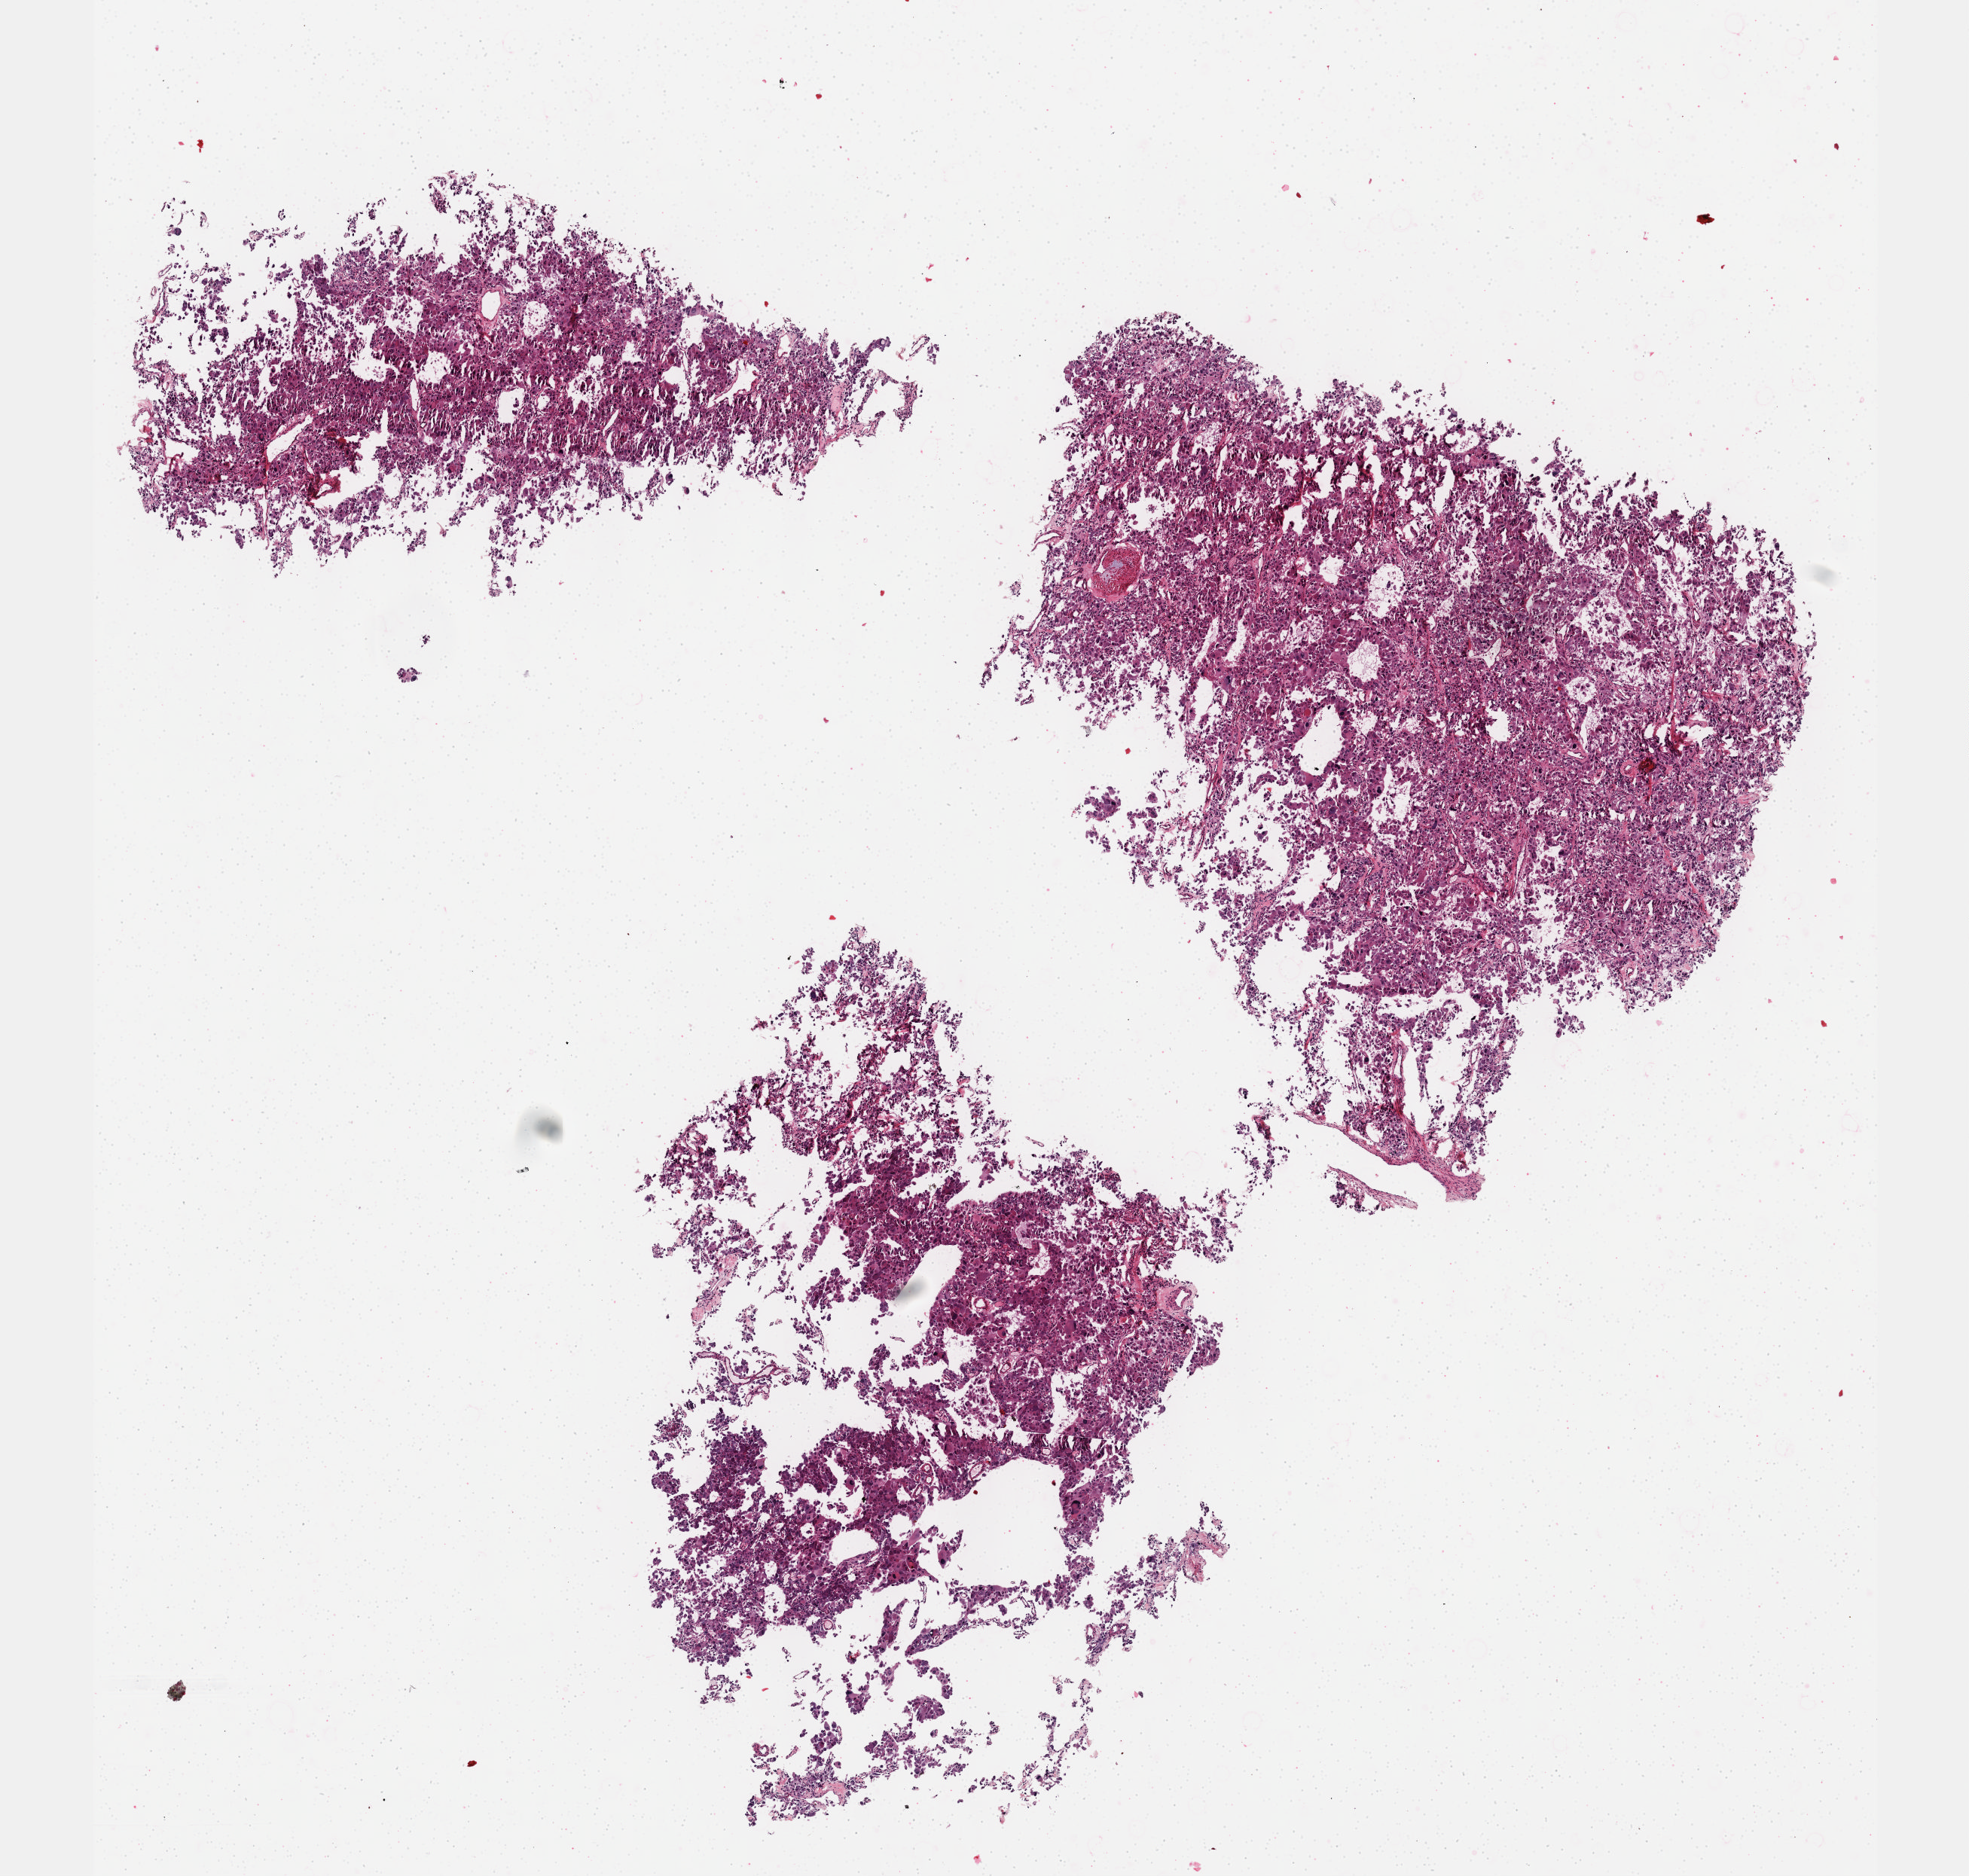
Digitized Hematoxylin and eosin (H&E) stained tissue section (whole slide) — low-resolution overview of the scanned area, about 10.6 x 10.1 mm; FFPE section; adrenal gland, primary tumour sample. Female, age 59 years at initial diagnosis.
- laterality: right
- diagnosis: Pheochromocytoma, NOS